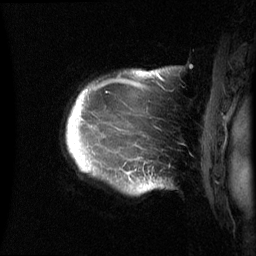
Breast MRI (dynamic contrast-enhanced), one sagittal slice. Position 55 of 60 along the scan axis. Dynamic contrast-enhanced series, image 2 of 3 at this slice position (ordered by acquisition). 1.5 T. TE 4.2 ms, TR 8.4 ms. 2.4 mm slice thickness. 256 × 256 image matrix, field of view 230 × 230 mm. Patient: female, 48 years.
Structures marked on this image (semi-automatically segmented with operator editing):
- analysis volume of interest (the breast-tissue region the enhancement analysis was run in; not a lesion): bounding box [x1, y1, x2, y2] px = [67, 70, 159, 194]
- tumour enhancement mask (voxels above the 70 % enhancement threshold inside the analysis volume of interest): [128, 71, 157, 174]